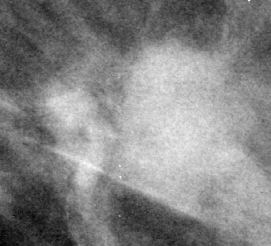
Cropped region of a digitized screen-film mammogram centred on a radiologist-marked abnormality, right breast, CC view.
Finding: mass, shape irregular / architectural distortion, margins microlobulated / ill defined / spiculated; BI-RADS assessment category 4; pathology (as recorded): malignant.